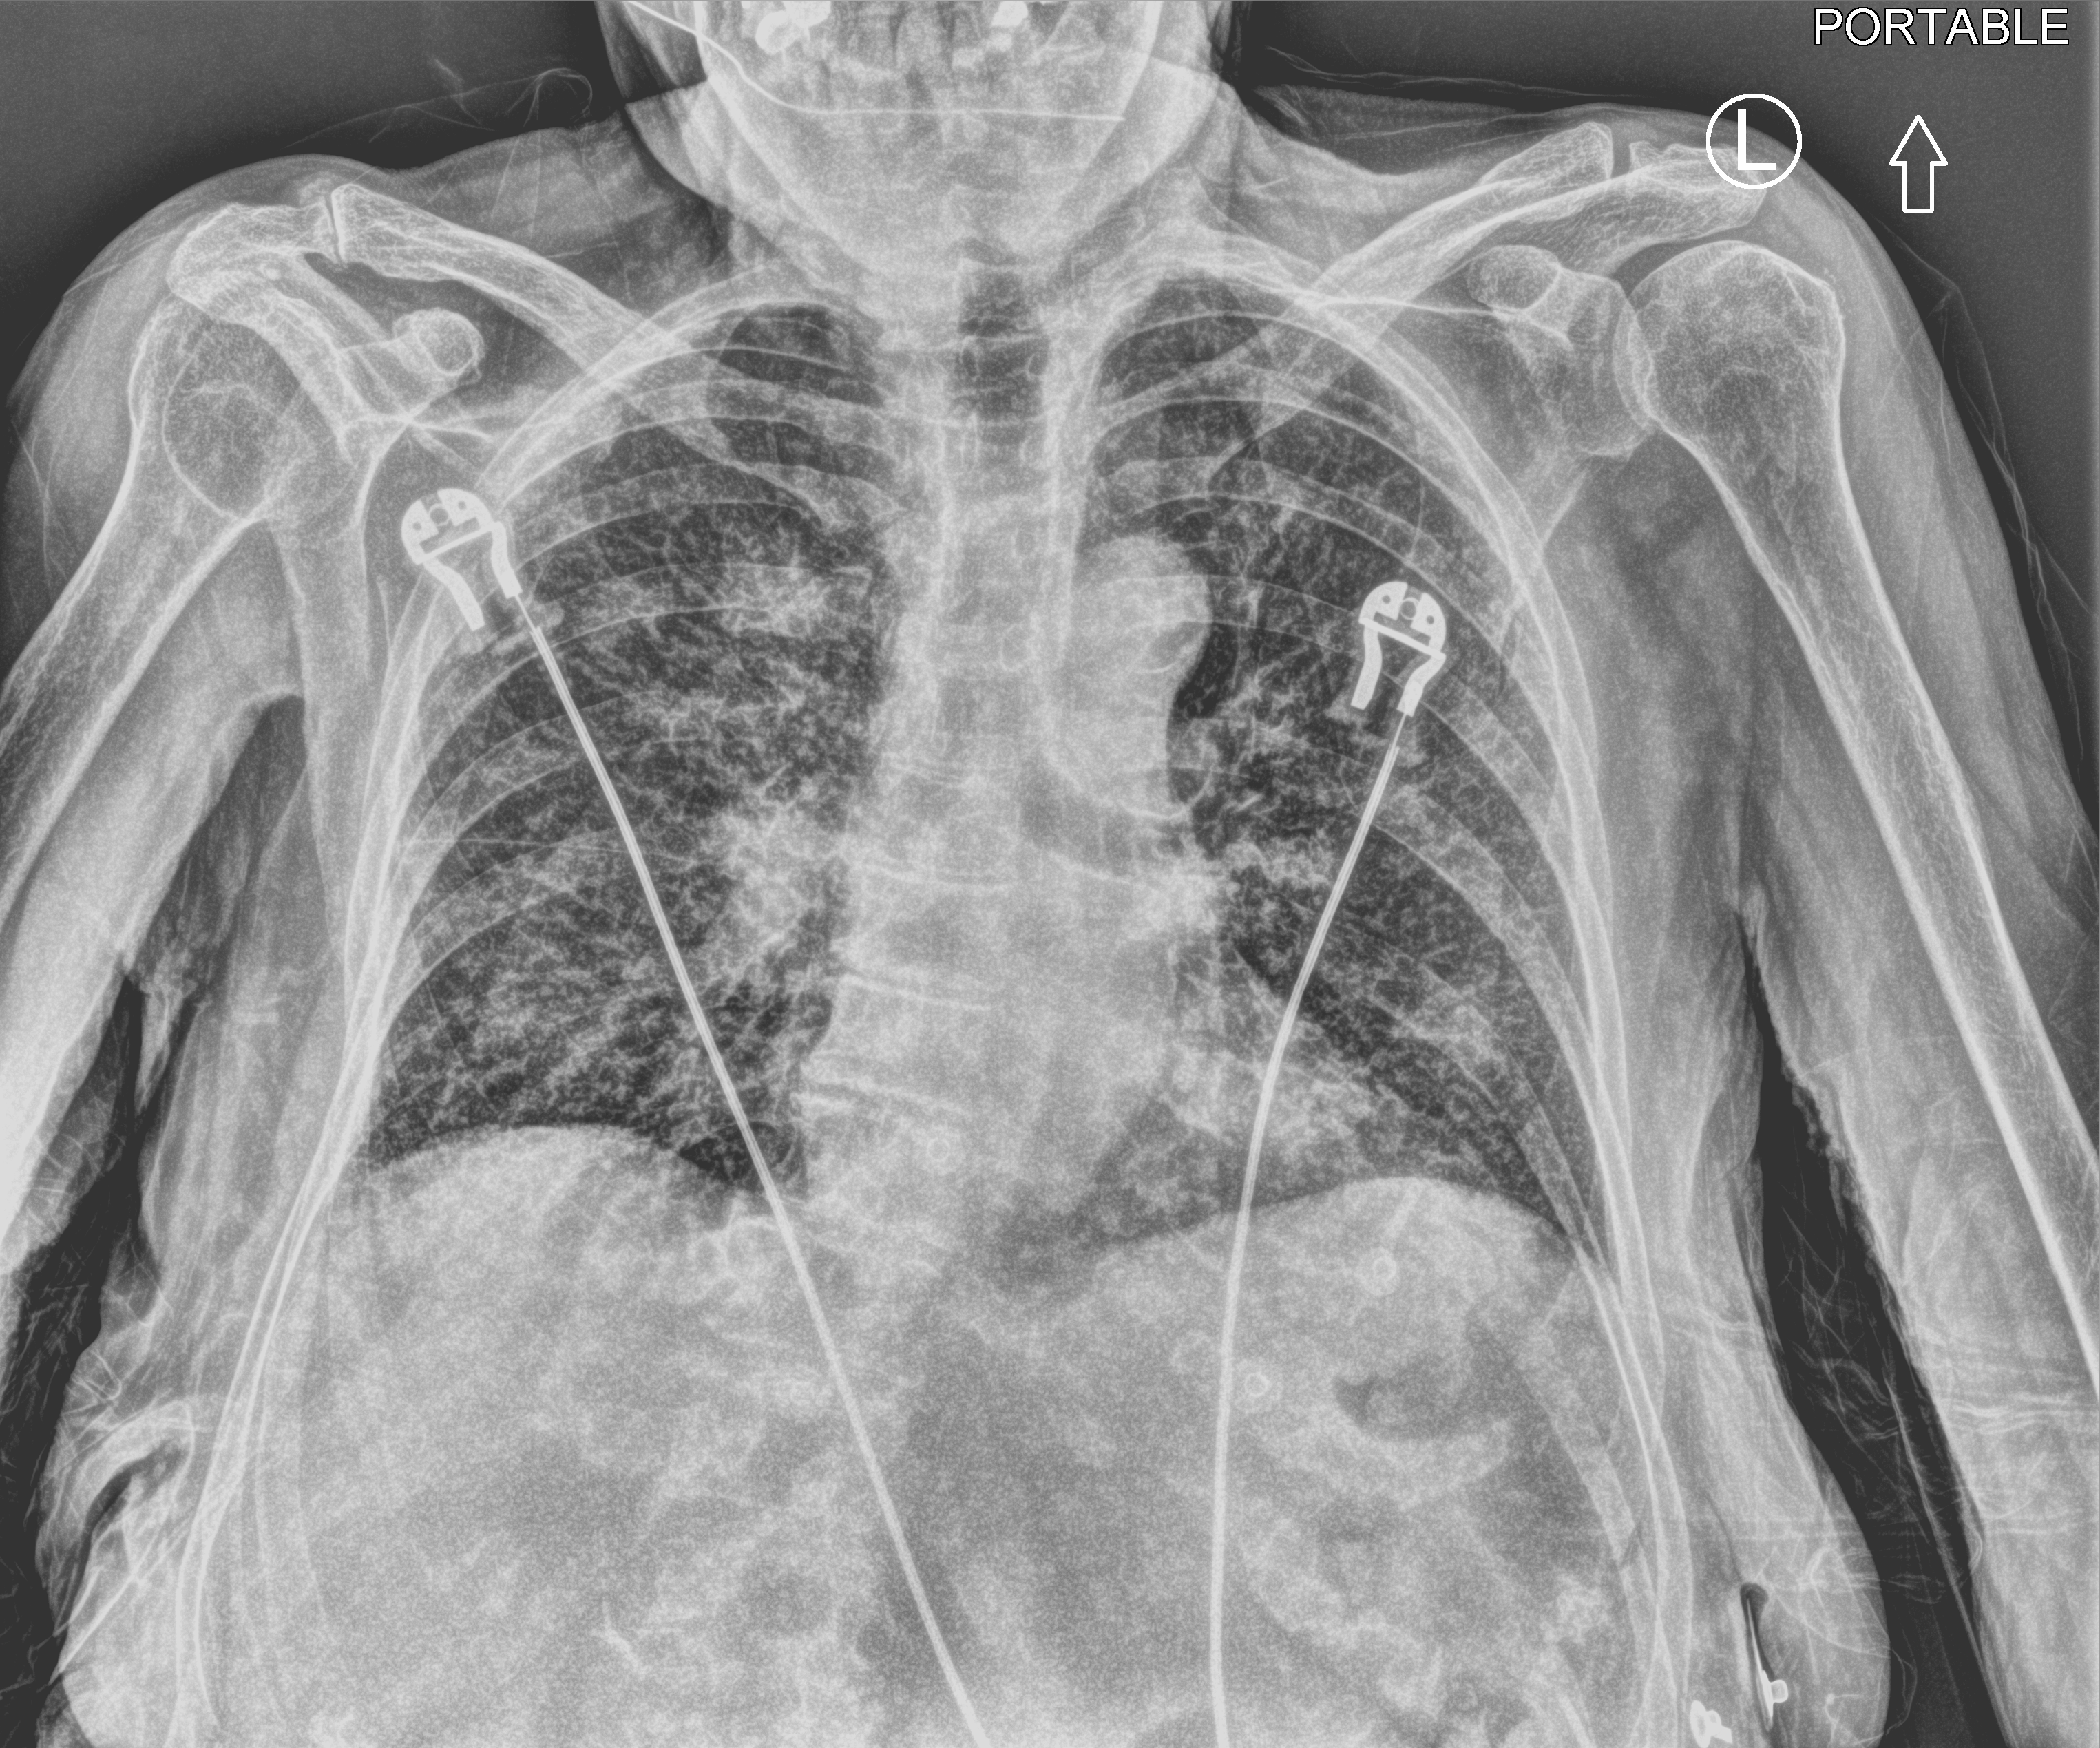
Bedside chest radiograph (computed radiography). Female patient hospitalised with COVID-19, age 75–90 years.
Hospital-stay facts (about this admission, not read from this image; timing relative to this image not recorded): chronic kidney disease (admission record): no; smoking status (admission record): never.